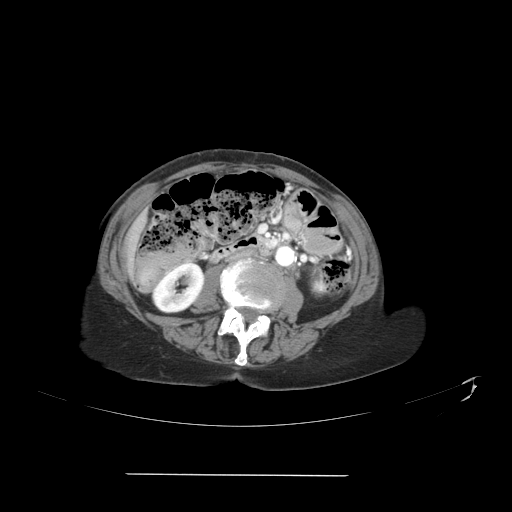
Contrast-enhanced abdominal CT, one axial slice; slice 10 of 41 in the series (ordered by position); reconstruction kernel STANDARD; 120 kVp; soft-tissue window (W 400 / L 40 HU); 5 mm slice thickness; 512 × 512 image matrix, field of view 431 × 431 mm. Female patient, age 74 years. From the clinical record (not read from this slice): diagnosis: colorectal cancer liver metastases, imaged before liver resection; multiple liver metastases: yes; largest metastasis: 3.3 cm.
Annotated regions visible in this slice (expert manual segmentation):
- liver: bounding box [x1, y1, x2, y2] px = [130, 241, 132, 254]